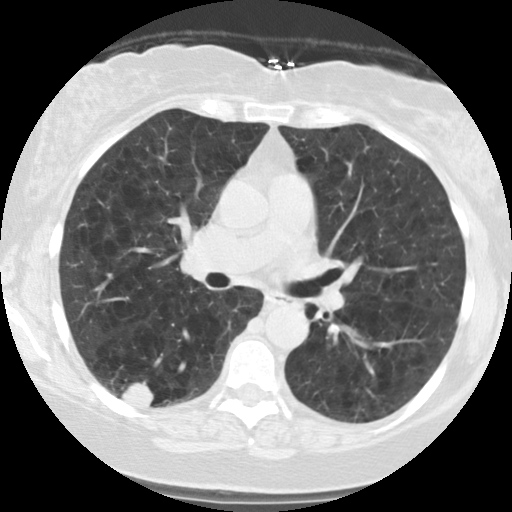
Chest CT (low-dose screening protocol), one axial image; second annual screen; lung window (W 1500 / L -600 HU); 2.5 mm slice thickness; 140 kVp; 512 × 512 image matrix, field of view 310 × 310 mm. Female participant, aged 59 years at enrolment.
• Expert-annotated lung lesion, bounding box [x1, y1, x2, y2] px = [106, 360, 175, 420].
• The screening reader recorded 2 non-calcified nodules or masses ≥4 mm on this exam (right lower lobe, right lower lobe); which of them this box marks is not recorded.
• Official screen result: positive, other.
• Later outcome: lung cancer diagnosed 63 days after this screen — squamous cell carcinoma, NOS, right lower lobe, poorly differentiated (G3), stage IB (AJCC 6th edition), 30 mm at pathology.